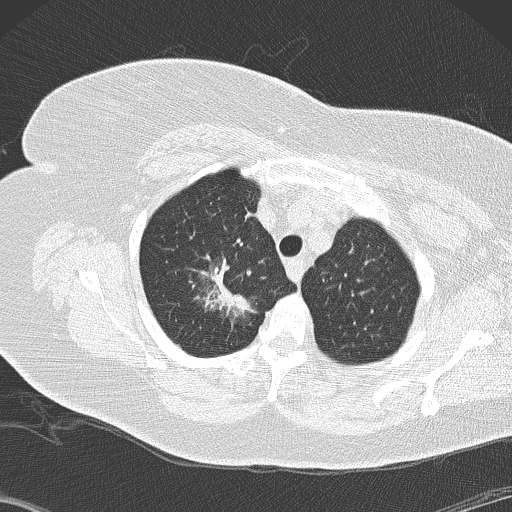
Low-dose screening chest CT, axial slice. Second screening round (one year after baseline). Lung window (W 1500 / L -600 HU). 2 mm slice thickness. Lung (sharp) reconstruction kernel (B50f). Slice 27 of 146 in the series. Female participant, aged 72 years at enrolment. Former smoker at enrolment.
• Expert-annotated lung lesion, bounding box (x1, y1, x2, y2) in pixels: (180, 243, 261, 328).
• The screening reader recorded 4 non-calcified nodules or masses ≥4 mm on this exam (right lower lobe, right lower lobe, right lower lobe, right upper lobe); which of them this box marks is not recorded.
• Lung cancer was diagnosed 52 days after this screen: bronchiolo-alveolar adenocarcinoma, NOS, right upper lobe, stage IIIB (AJCC 6th edition), 45 mm at pathology.